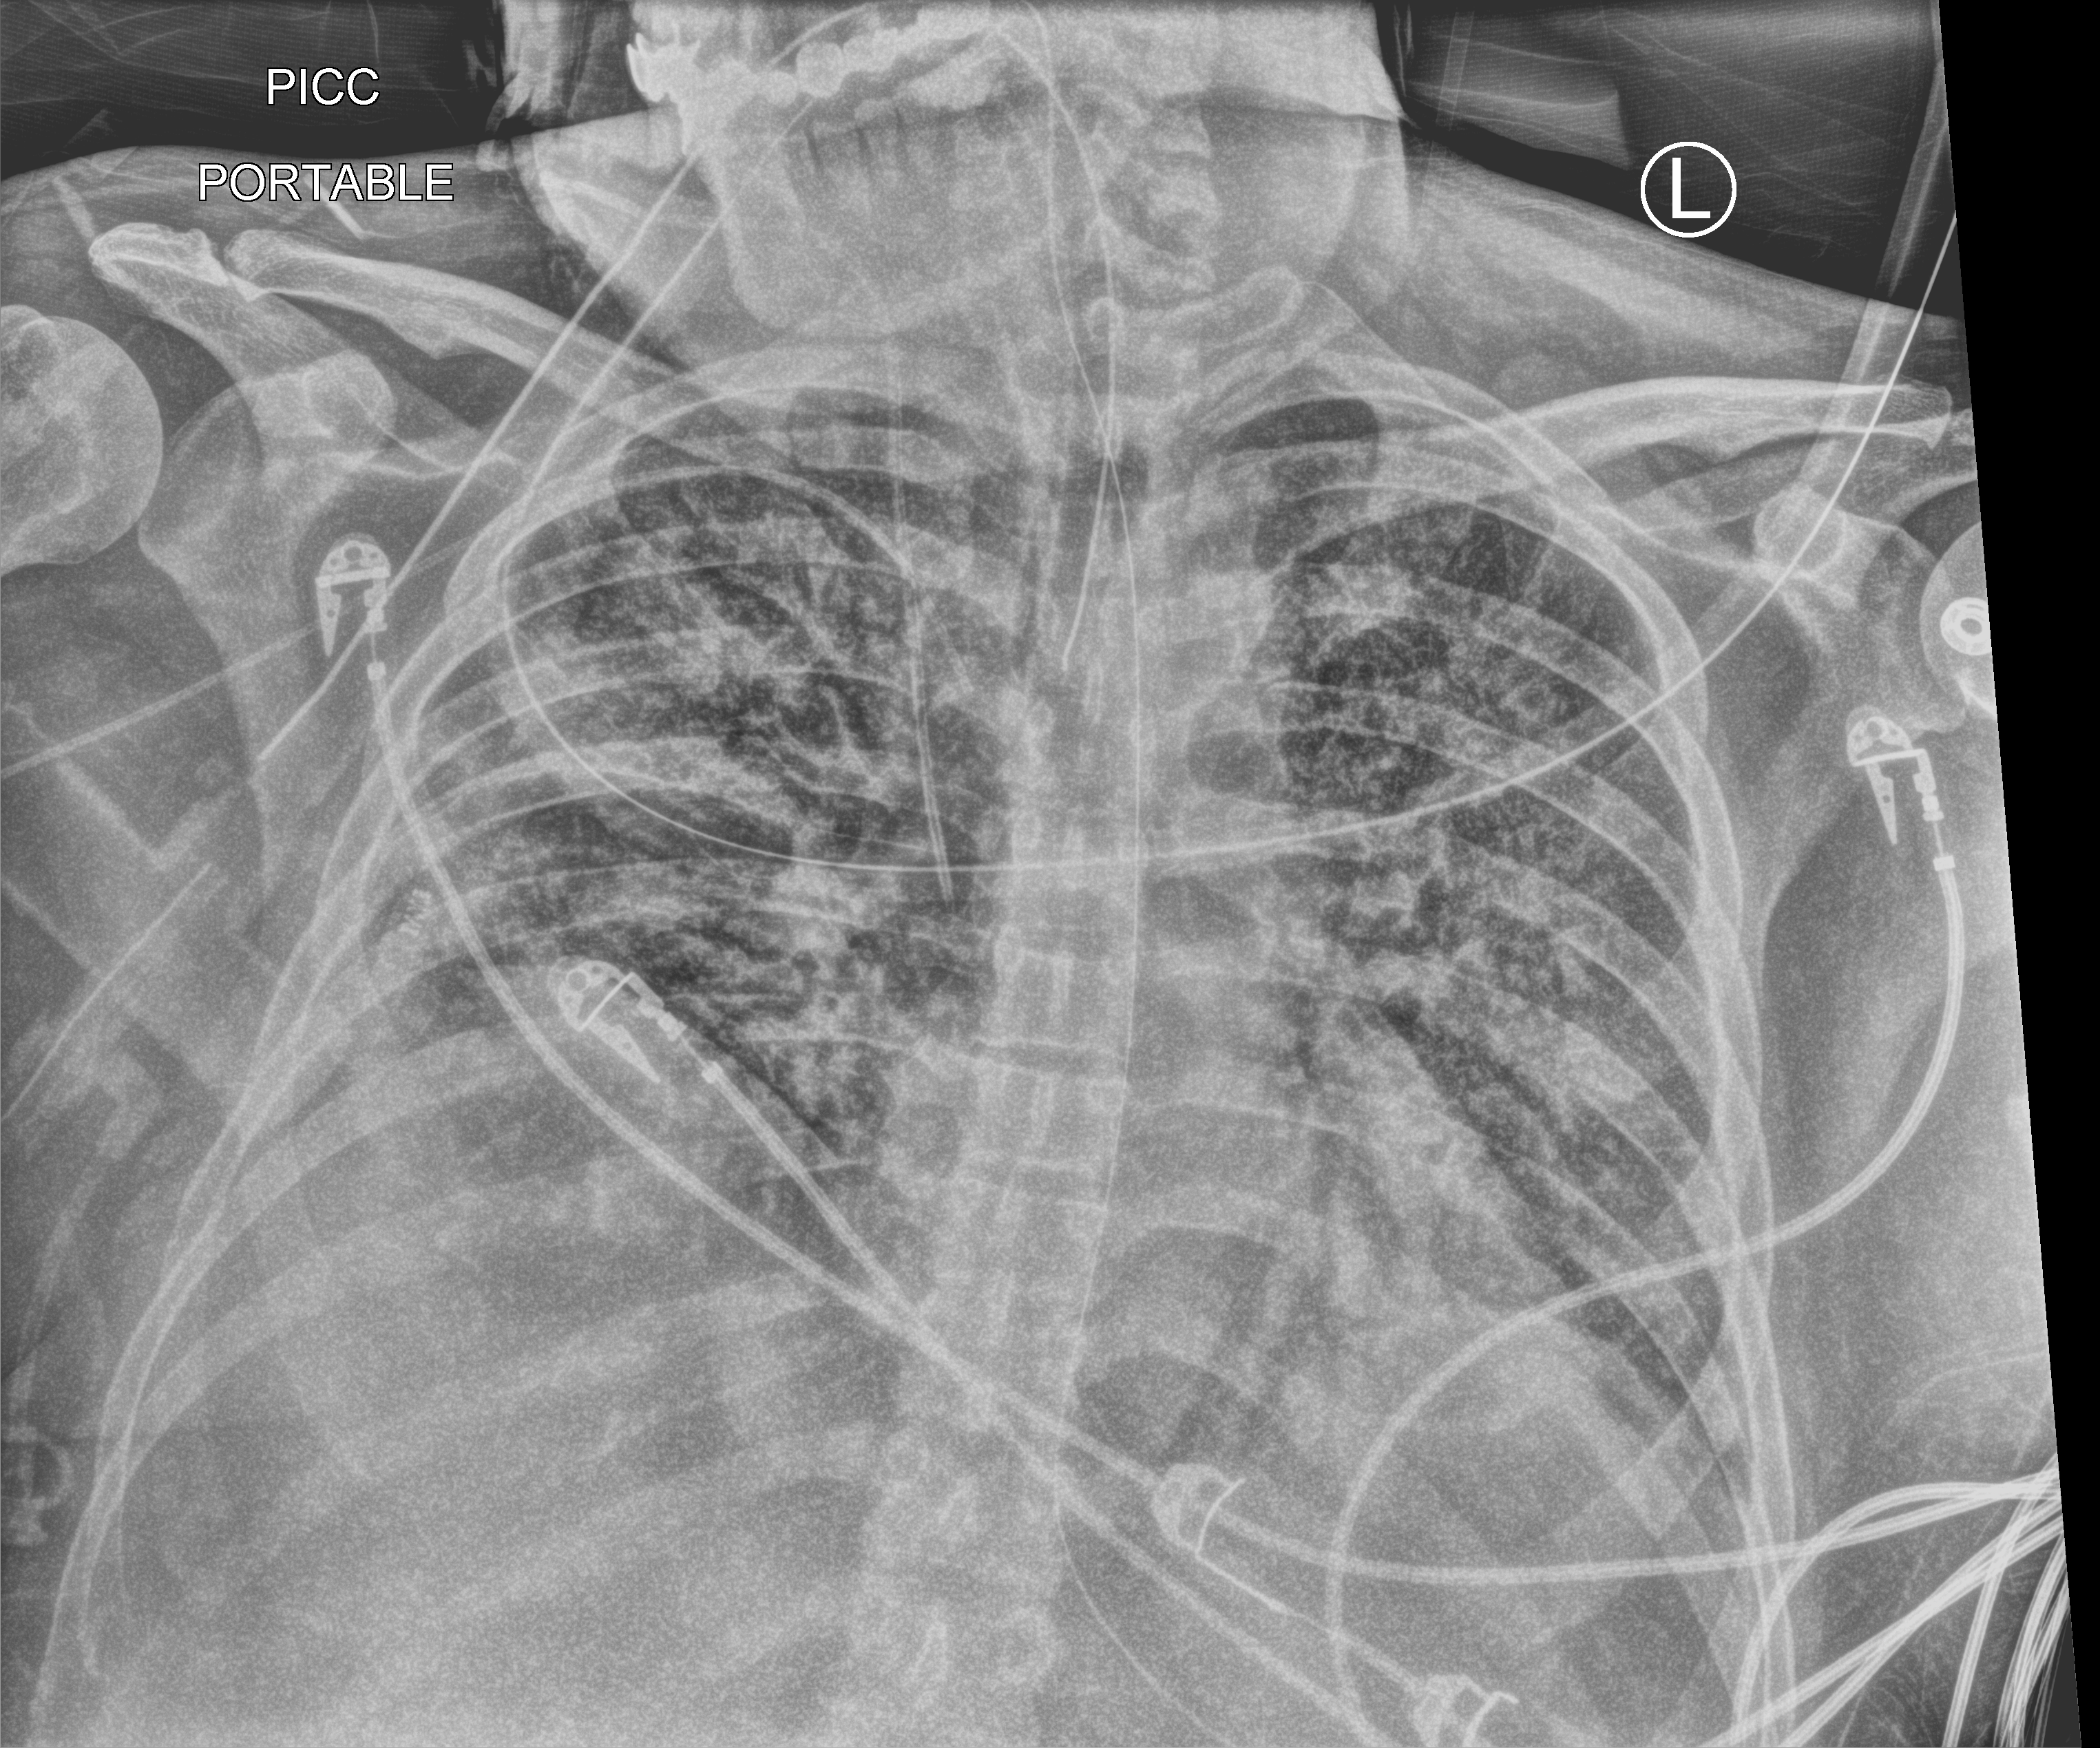
Chest X-ray (portable), anteroposterior (AP) projection. Patient hospitalised with COVID-19; male, aged 18–59 years.
Admission-level facts for this patient (not findings on this image; timing relative to this image not recorded):
- smoking status (admission record): never
- mechanically ventilated during this hospital stay: yes